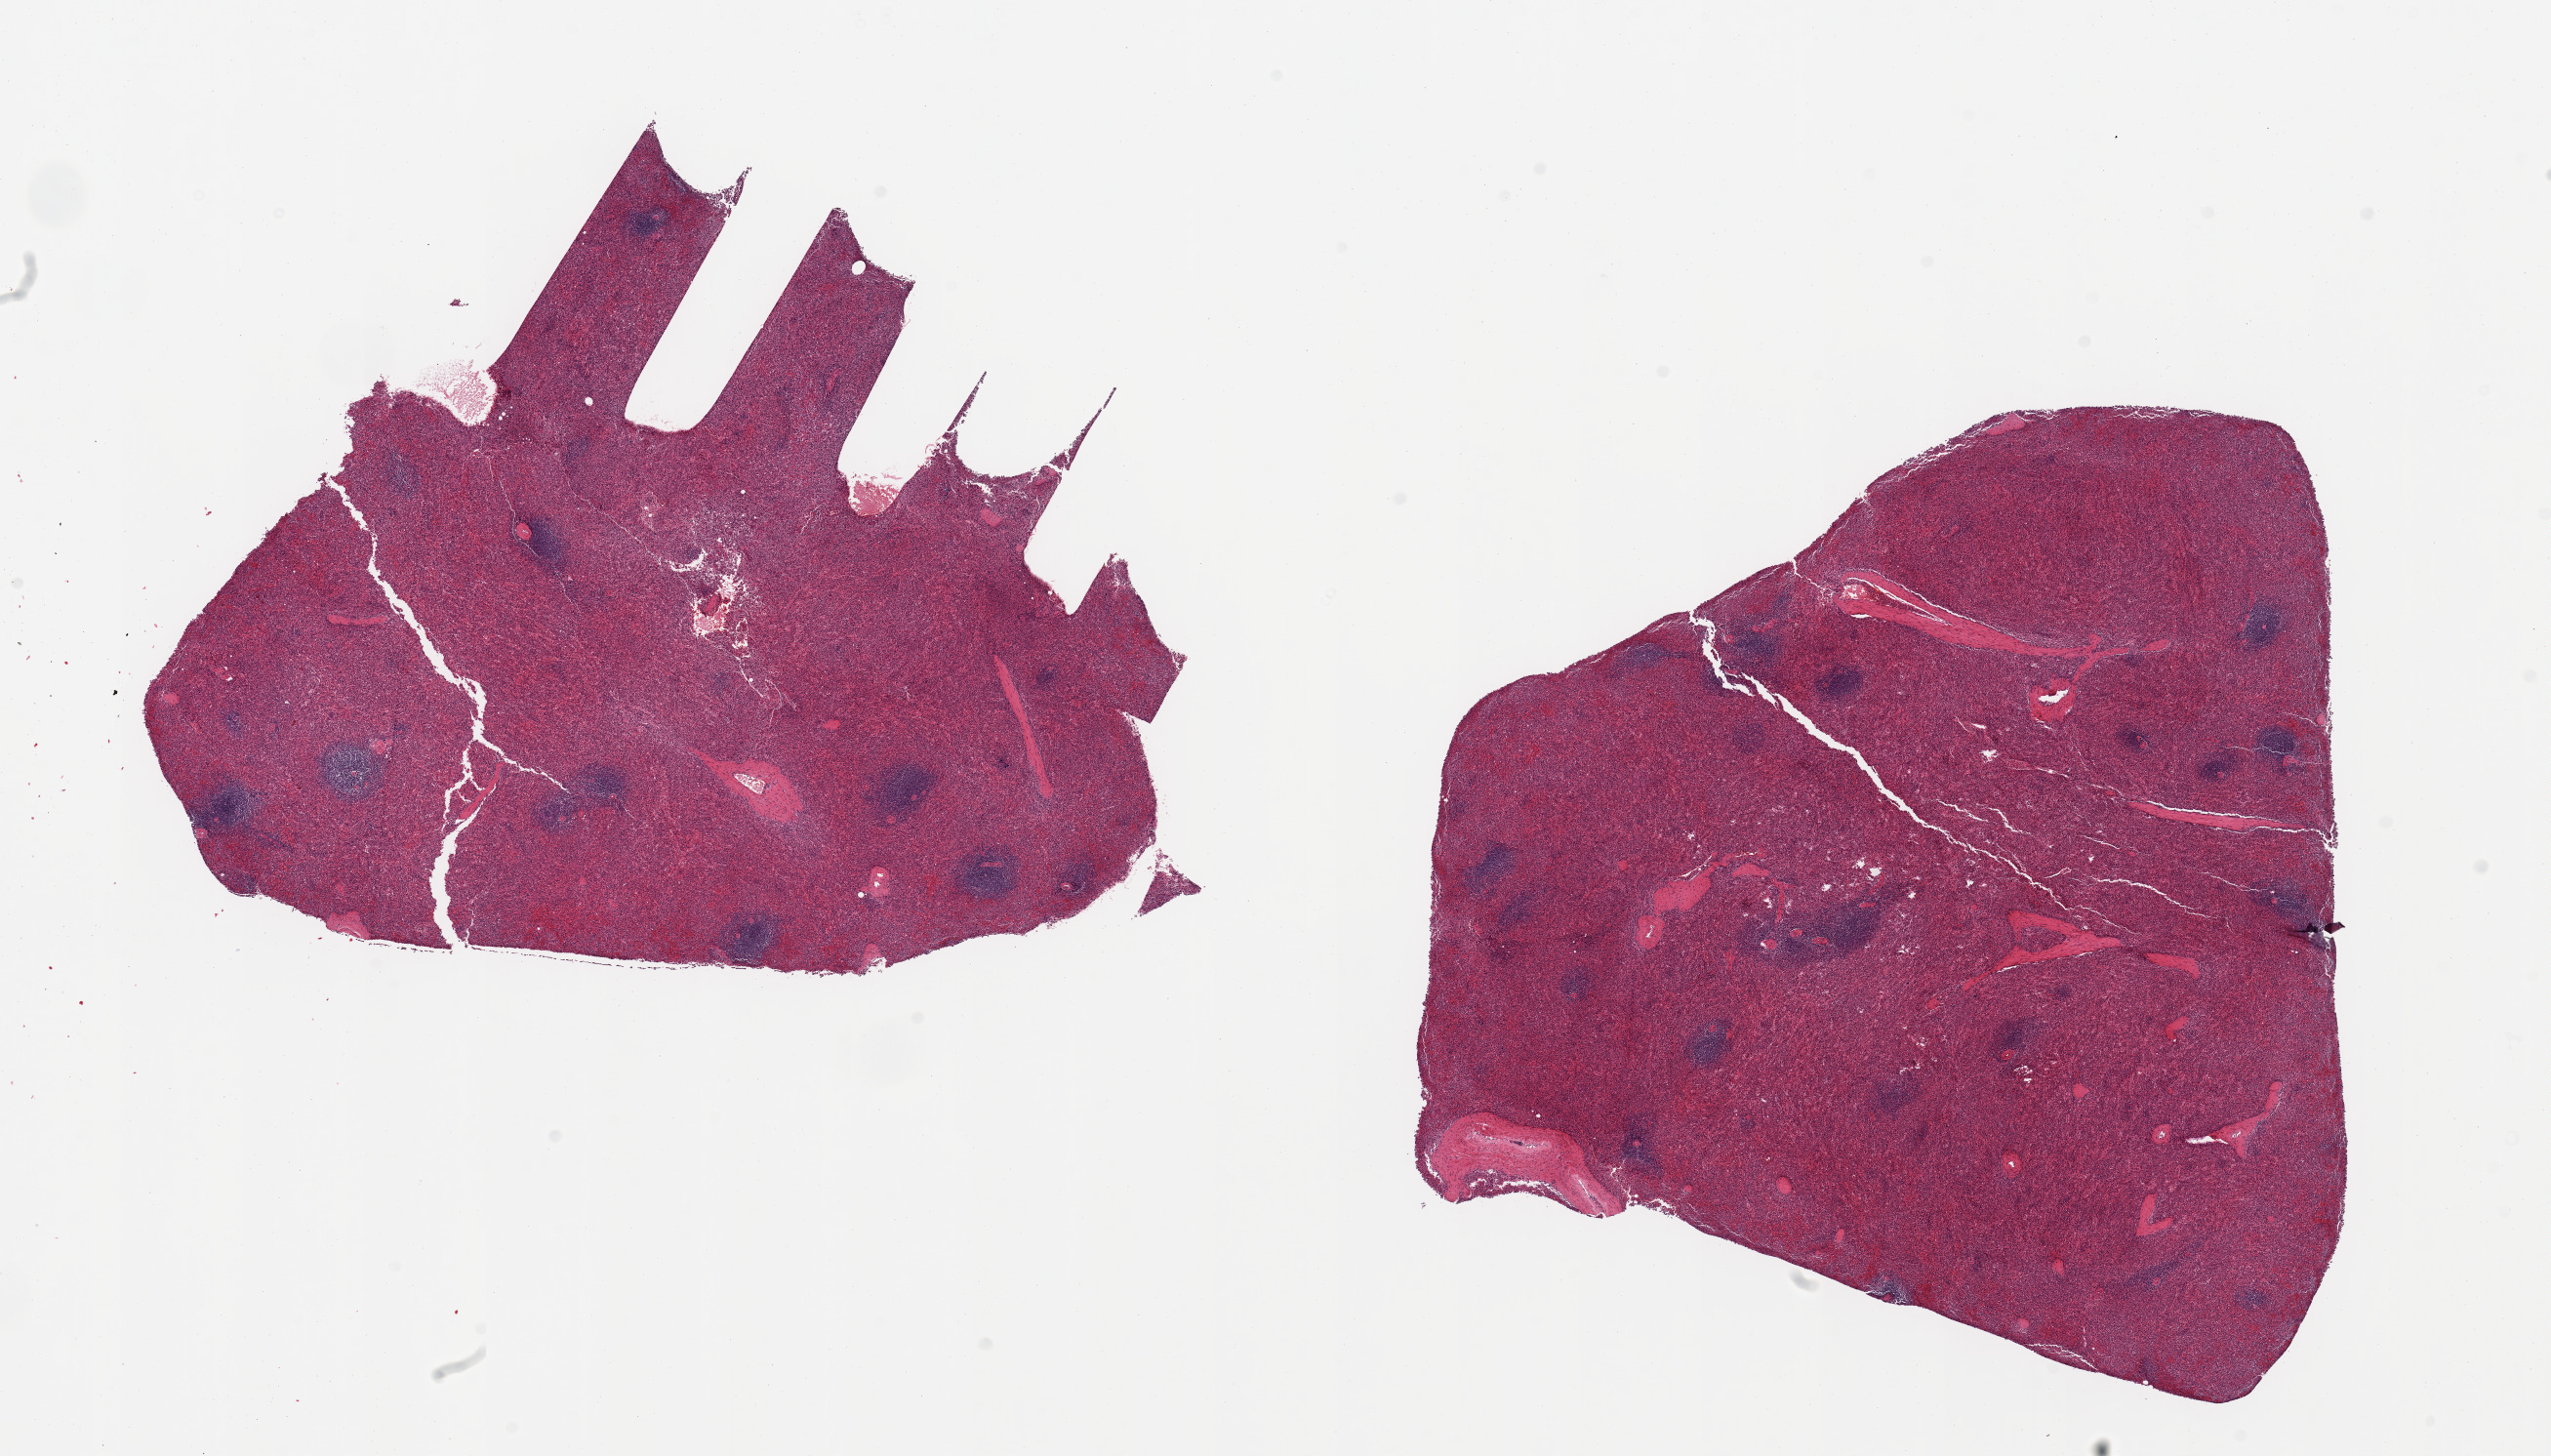
Hematoxylin and eosin (H&E) whole-slide image — low-resolution overview of the scanned area, about 20.7 x 11.8 mm. PAXgene-fixed, paraffin-embedded tissue. Target tissue: spleen. Tissue donor sample. Donor sex: male.
Review note (as recorded): 2 pieces, no abnormalities.